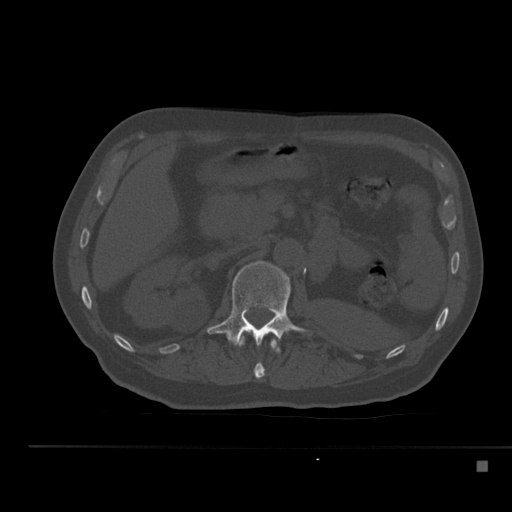
CT including the spine, one axial slice; reconstruction kernel Br40s; bone window (W 1800 / L 400 HU); 1.5 mm slice thickness; 512 × 512 image matrix, field of view 408 × 408 mm. Patient: male, 70 years. Case-level facts recorded for this patient, not image findings: primary cancer: renal.
Structures marked on this image (semi-automatically segmented with operator editing):
- L1 vertebra: bounding box <207,261,307,346> (left, top, right, bottom; pixels)
- T12 vertebra: <239,336,281,379>